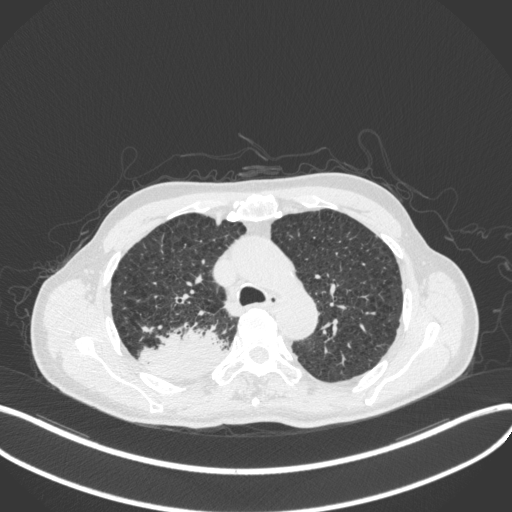
Chest CT, one axial slice; position 323 of 423 along the scan axis; 120 kVp; lung window (W 1500 / L -600 HU); 1 mm slice thickness; 512 × 512 image matrix, field of view 400 × 400 mm. Patient: male, 79 years. Case-level facts recorded for this patient, not image findings: clinical TNM (as recorded): T3 N0 M0.
Structures marked on this image (rectangle marked by the reading radiologist):
- lung tumour (recorded histology: adenocarcinoma): bounding box <139,326,229,380> (left, top, right, bottom; pixels)